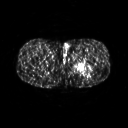
FDG PET of an extremity soft-tissue mass (from a PET/CT study), one axial slice; position 249 of 267 along the scan axis; 3.27 mm slice thickness; 128 × 128 image matrix, field of view 500 × 500 mm. Male patient, age 27 years. Case-level facts recorded for this patient, not image findings: histological type: extraskeletal osteosarcoma; grade: high; site of the primary tumour: left adductur.
Outlined on this slice (expert contour drawn on MRI and transferred to this co-registered scan by the dataset authors):
- gross tumour volume (mass): bounding box [x1, y1, x2, y2] px = [71, 57, 95, 74]